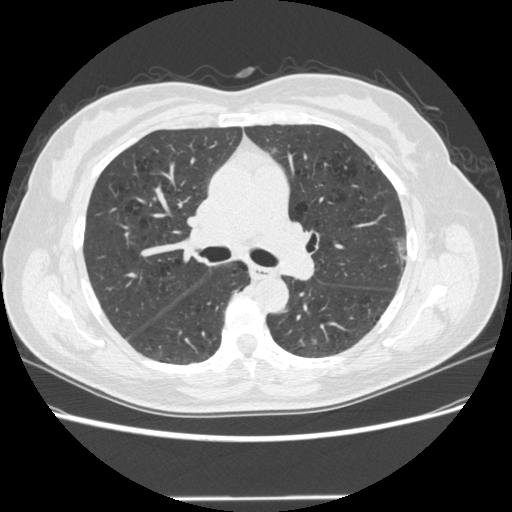
Chest CT (low-dose screening protocol), one axial image, baseline annual screen, lung window (W 1500 / L -600 HU), 1.25 mm slice thickness, standard (soft-tissue) reconstruction kernel (STANDARD), slice 192 of 301 in the series, 512 × 512 image matrix, field of view 360 × 360 mm. Female, age 61 years at enrolment.
- Expert reader's lesion annotation, bounding box <382,227,425,278> (left, top, right, bottom; pixels).
- Screening reader's record for this exam: no non-calcified nodule ≥4 mm recorded.
- Official screen result: negative screen, minor abnormalities not suspicious for lung cancer.
- Later outcome: lung cancer diagnosed 791 days after this screen — bronchiolo-alveolar adenocarcinoma, NOS, left upper lobe, well differentiated (G1), stage IA (AJCC 6th edition), 11 mm at pathology.